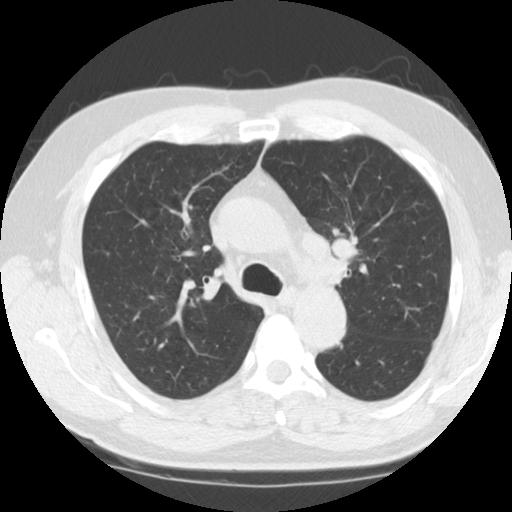
Low-dose screening chest CT, one axial slice; slice 87 of 124 in the series (ordered by position); reconstruction kernel STANDARD; lung window (W 1500 / L -600 HU); 2.5 mm slice thickness; 512 × 512 image matrix.
Annotated regions visible in this slice (manually delineated by an expert):
- lesion 1 (tumor, upper lobe of left lung): bounding box (x1, y1, x2, y2) in pixels: (331, 238, 358, 261)